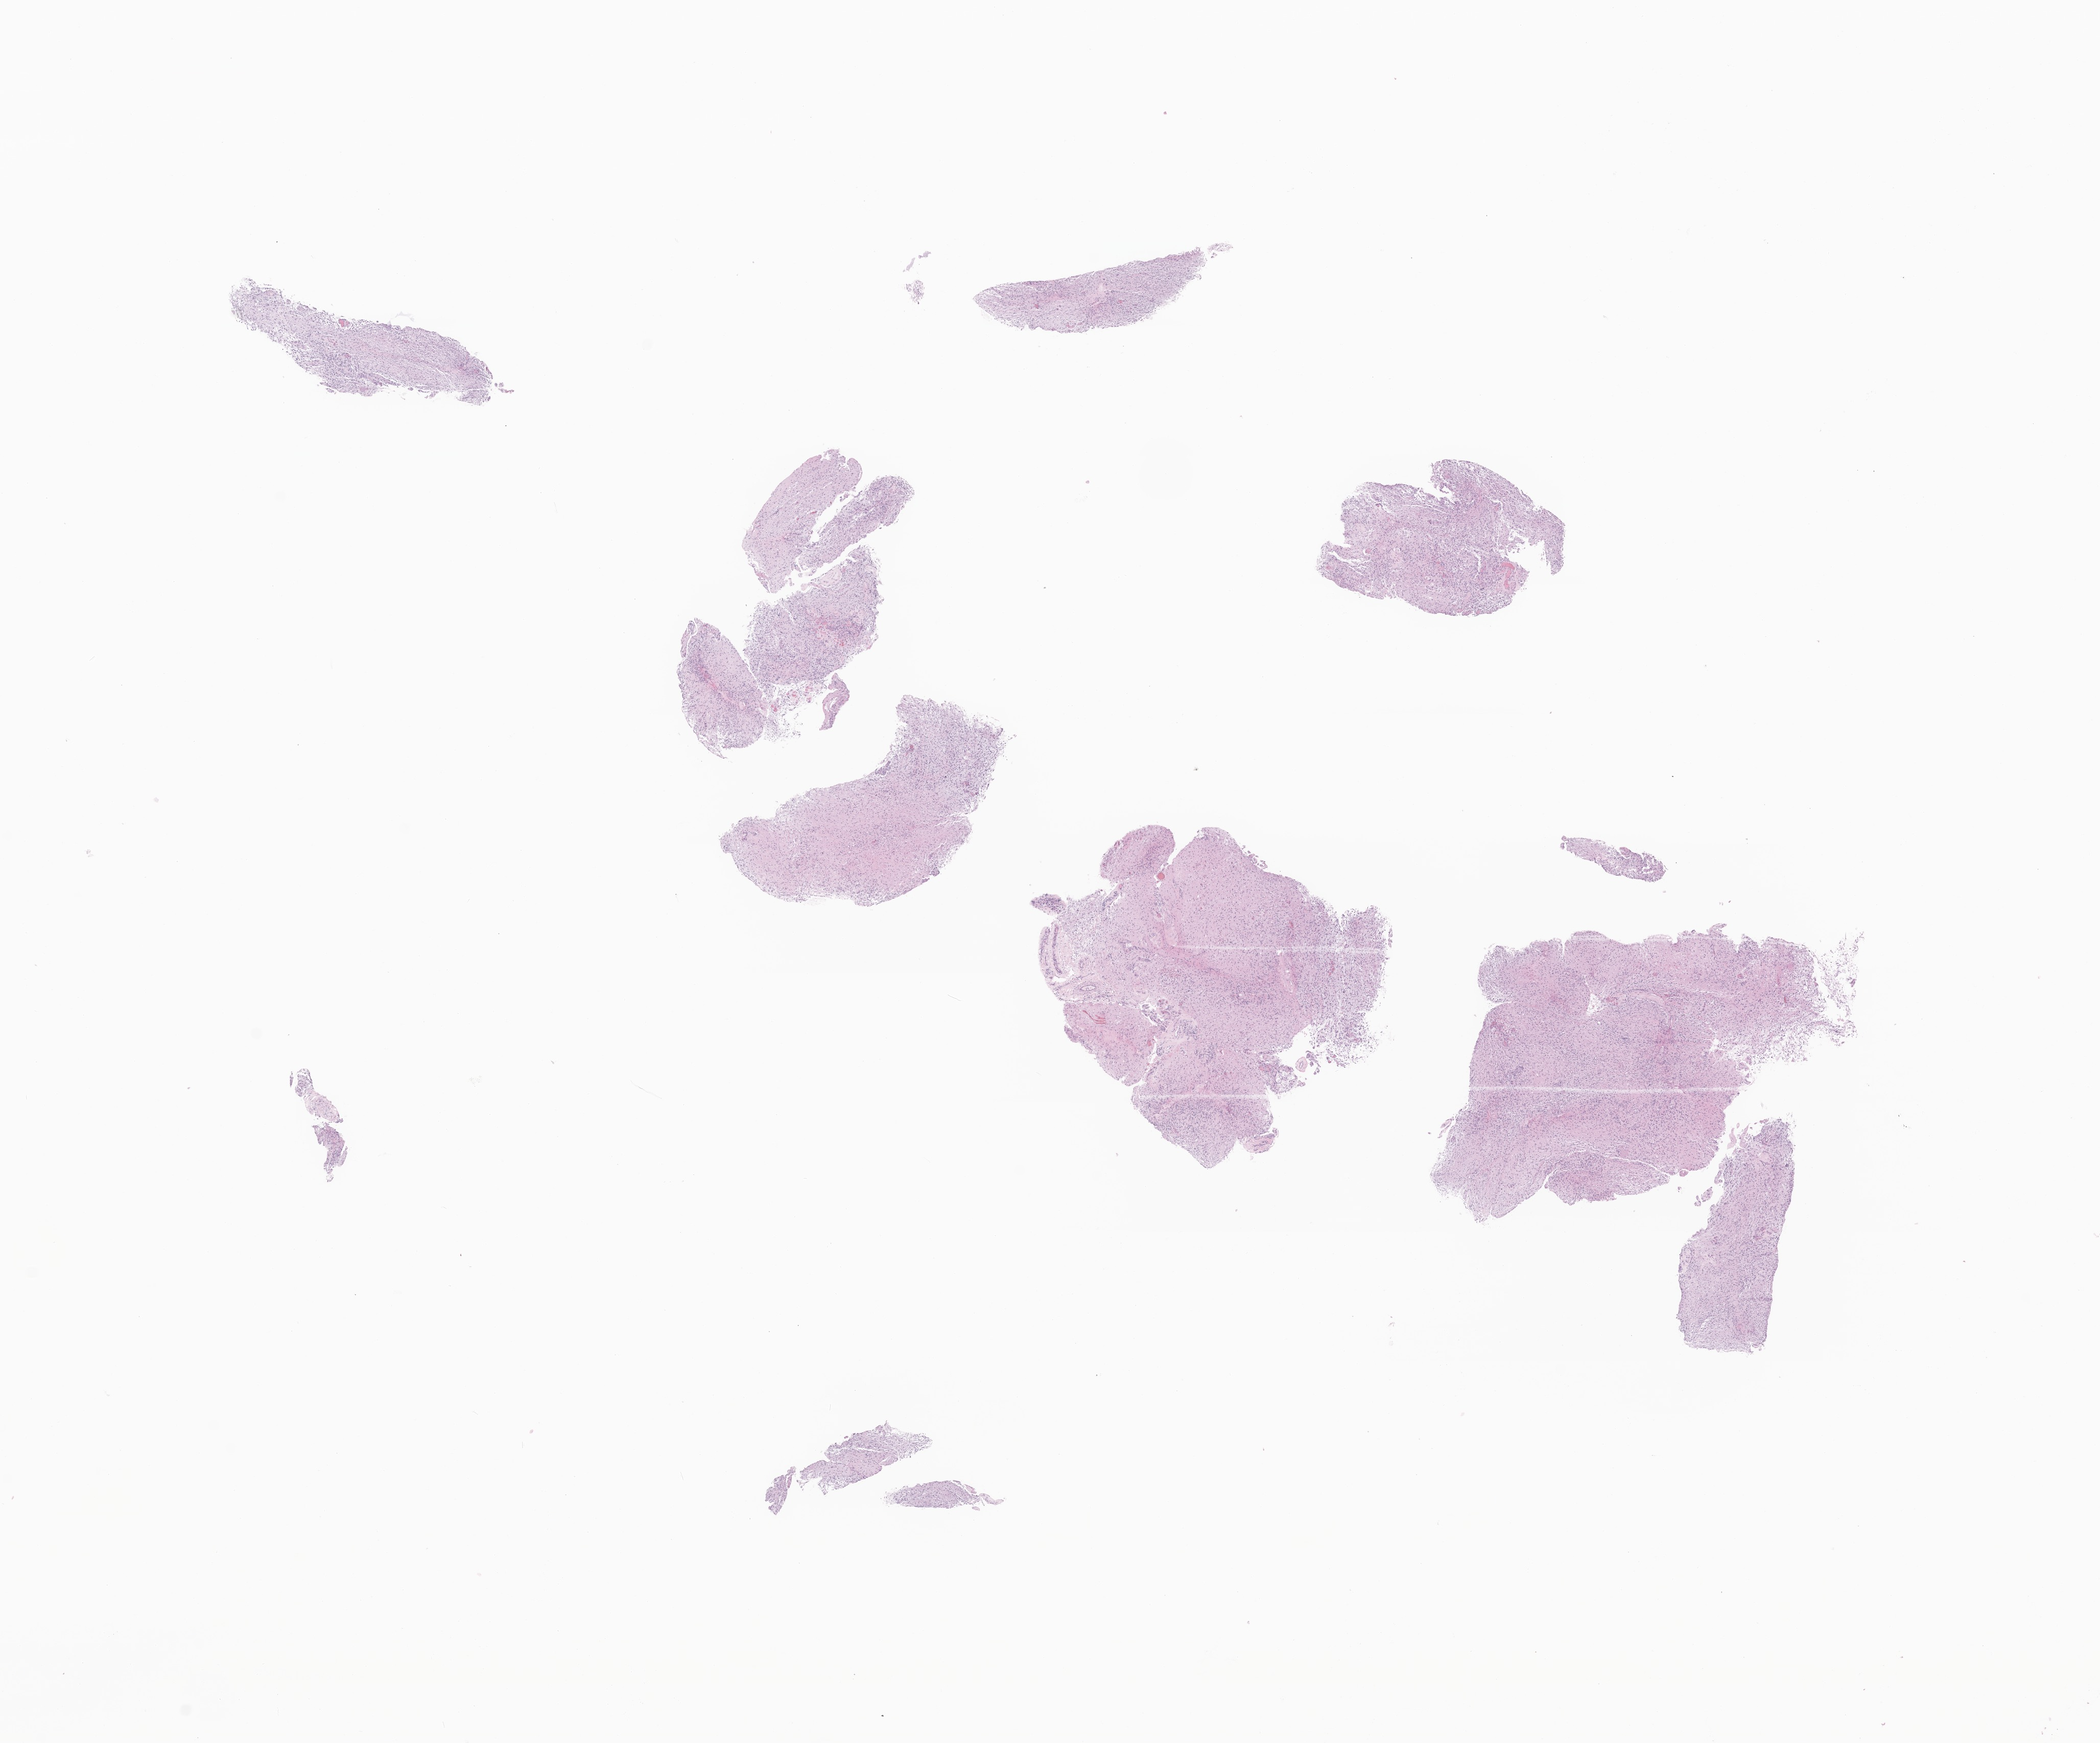
Whole-slide image, hematoxylin and eosin (H&E) stain of tumor tissue from the spinal cord, whole scanned area (about 17.3 x 14.4 mm) shown as a low-resolution overview, FFPE section. Patient male; age 90 months.
* diagnosis (ICD-O-3 morphology term): Pilocytic astrocytoma